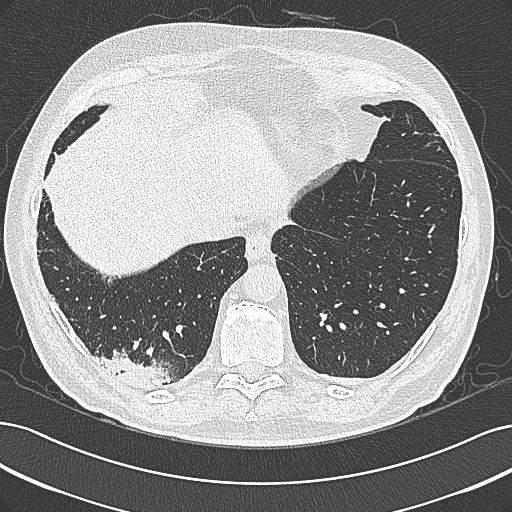
Axial slice from a low-dose chest CT screening exam, baseline screening round, lung window (W 1500 / L -600 HU), 1 mm slice thickness, lung (sharp) reconstruction kernel (B80f). Male participant, aged 68 years at enrolment. Former smoker at enrolment.
Expert reader's lesion annotation, box from (x=97, y=341) to (x=185, y=402) px. No non-calcified nodule or mass ≥4 mm was recorded by the screening reader at this exam. Lung cancer was diagnosed 154 days after this screen: mucinous adenocarcinoma, right lower lobe, well differentiated (G1), stage IB (AJCC 6th edition), 50 mm at pathology.